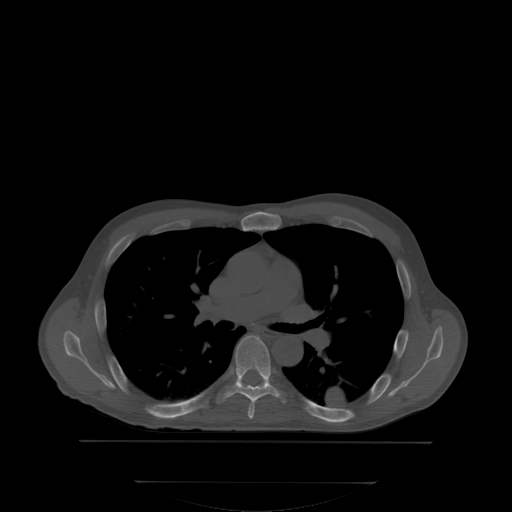
CT including the spine, one axial slice; slice 238 of 350 in the series (ordered by position); bone window (W 1800 / L 400 HU); 2.5 mm slice thickness; 512 × 512 image matrix, field of view 500 × 500 mm. Patient: male, 58 years. Case-level facts recorded for this patient, not image findings: primary cancer: prostate.
Annotated regions visible in this slice (semi-automatic segmentation, software-assisted and operator-edited):
- T5 vertebra: box from (x=251, y=403) to (x=254, y=409) px
- T6 vertebra: (x=226, y=335)–(x=284, y=416)
- T7 vertebra: (x=241, y=383)–(x=269, y=385)